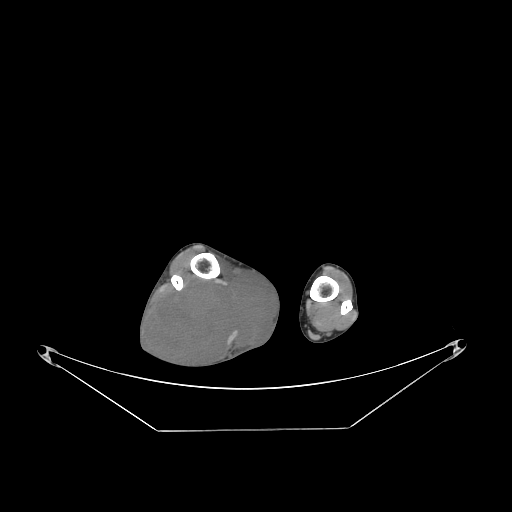
CT of an extremity soft-tissue mass (from a PET/CT study), one axial slice; slice 63 of 267 in the series (ordered by position); 140 kVp; soft-tissue window (W 400 / L 40 HU); 3.75 mm slice thickness; 512 × 512 image matrix. Male patient. From the clinical record (not read from this slice): histological type: liposarcoma - round cell; grade: high; site of the primary tumour: right calf.
Structures marked on this image (expert contour drawn on MRI and transferred to this co-registered scan by the dataset authors):
- gross tumour volume (mass): bounding box (x1, y1, x2, y2) in pixels: (151, 269, 279, 369)